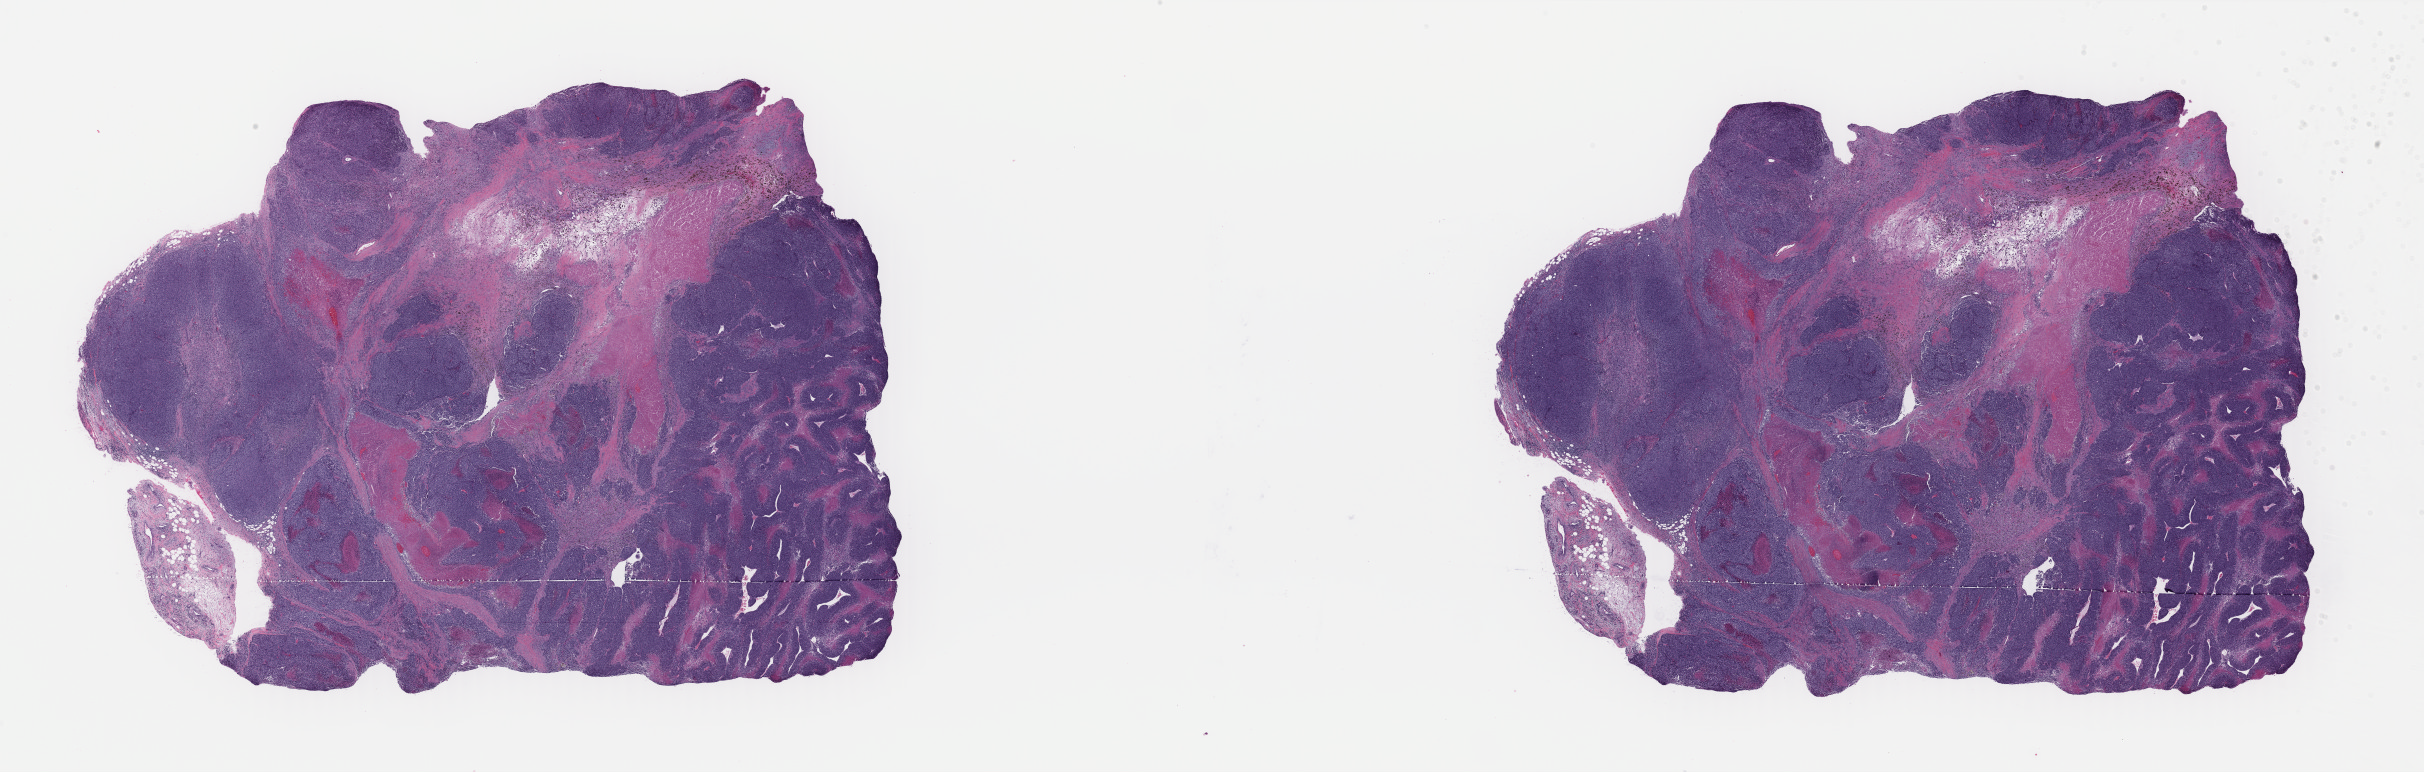
H&E-stained whole-slide image — shown as a low-resolution overview of the whole scanned area (about 38.4 x 12.2 mm), formalin-fixed paraffin-embedded (FFPE) diagnostic section, primary tumour sample from the skin. Patient: male, age at initial diagnosis 50 years.
• diagnosis: Malignant melanoma, NOS